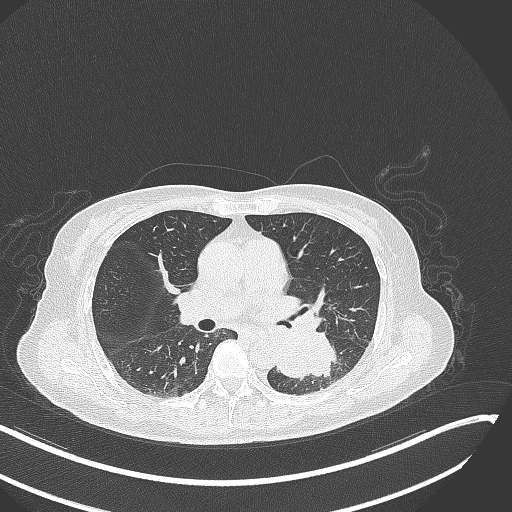
Chest CT, one axial slice; position 154 of 342 along the scan axis; reconstruction kernel B70f; lung window (W 1500 / L -600 HU); 512 × 512 image matrix. Female patient, age 64 years. Case-level facts recorded for this patient, not image findings: clinical TNM (as recorded): T3 N1 M1; histopathological grade: G3.
Outlined on this slice (rectangle marked by the reading radiologist):
- lung tumour (recorded histology: small cell carcinoma): bounding box (x1, y1, x2, y2) in pixels: (274, 326, 341, 378)